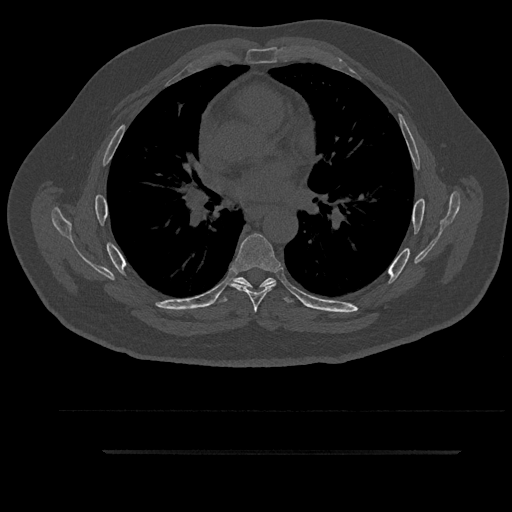
CT including the spine, one axial slice; slice 563 of 797 in the series (ordered by position); bone window (W 1800 / L 400 HU); 0.5 mm slice thickness; 512 × 512 image matrix, field of view 432 × 432 mm. Patient: male, 63 years. Case-level facts recorded for this patient, not image findings: primary cancer: renal.
Structures marked on this image (semi-automatic segmentation, software-assisted and operator-edited):
- T5 vertebra: bounding box (x1, y1, x2, y2) in pixels: (235, 278, 266, 291)
- T6 vertebra: (231, 234, 281, 312)
- T7 vertebra: (216, 277, 292, 303)